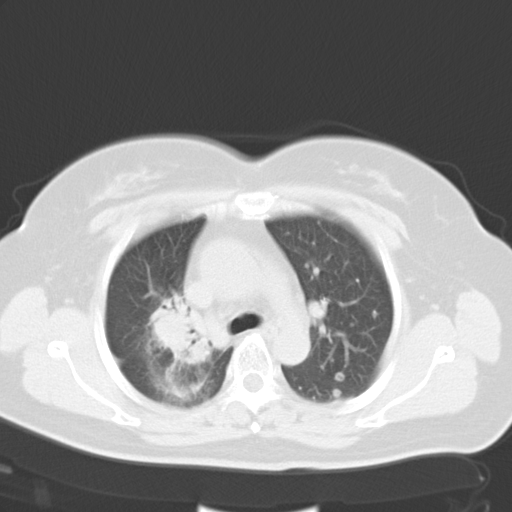
Chest CT, one axial slice; slice 22 of 30 in the series (ordered by position); 120 kVp; lung window (W 1500 / L -600 HU); 8 mm slice thickness; 512 × 512 image matrix, field of view 353 × 353 mm. Female patient, age 50 years. From the clinical record (not read from this slice): clinical TNM (as recorded): T2a N0 M1a.
Outlined on this slice (bounding box drawn by a radiologist):
- lung tumour (recorded histology: adenocarcinoma): bounding box <149,288,216,371> (left, top, right, bottom; pixels)